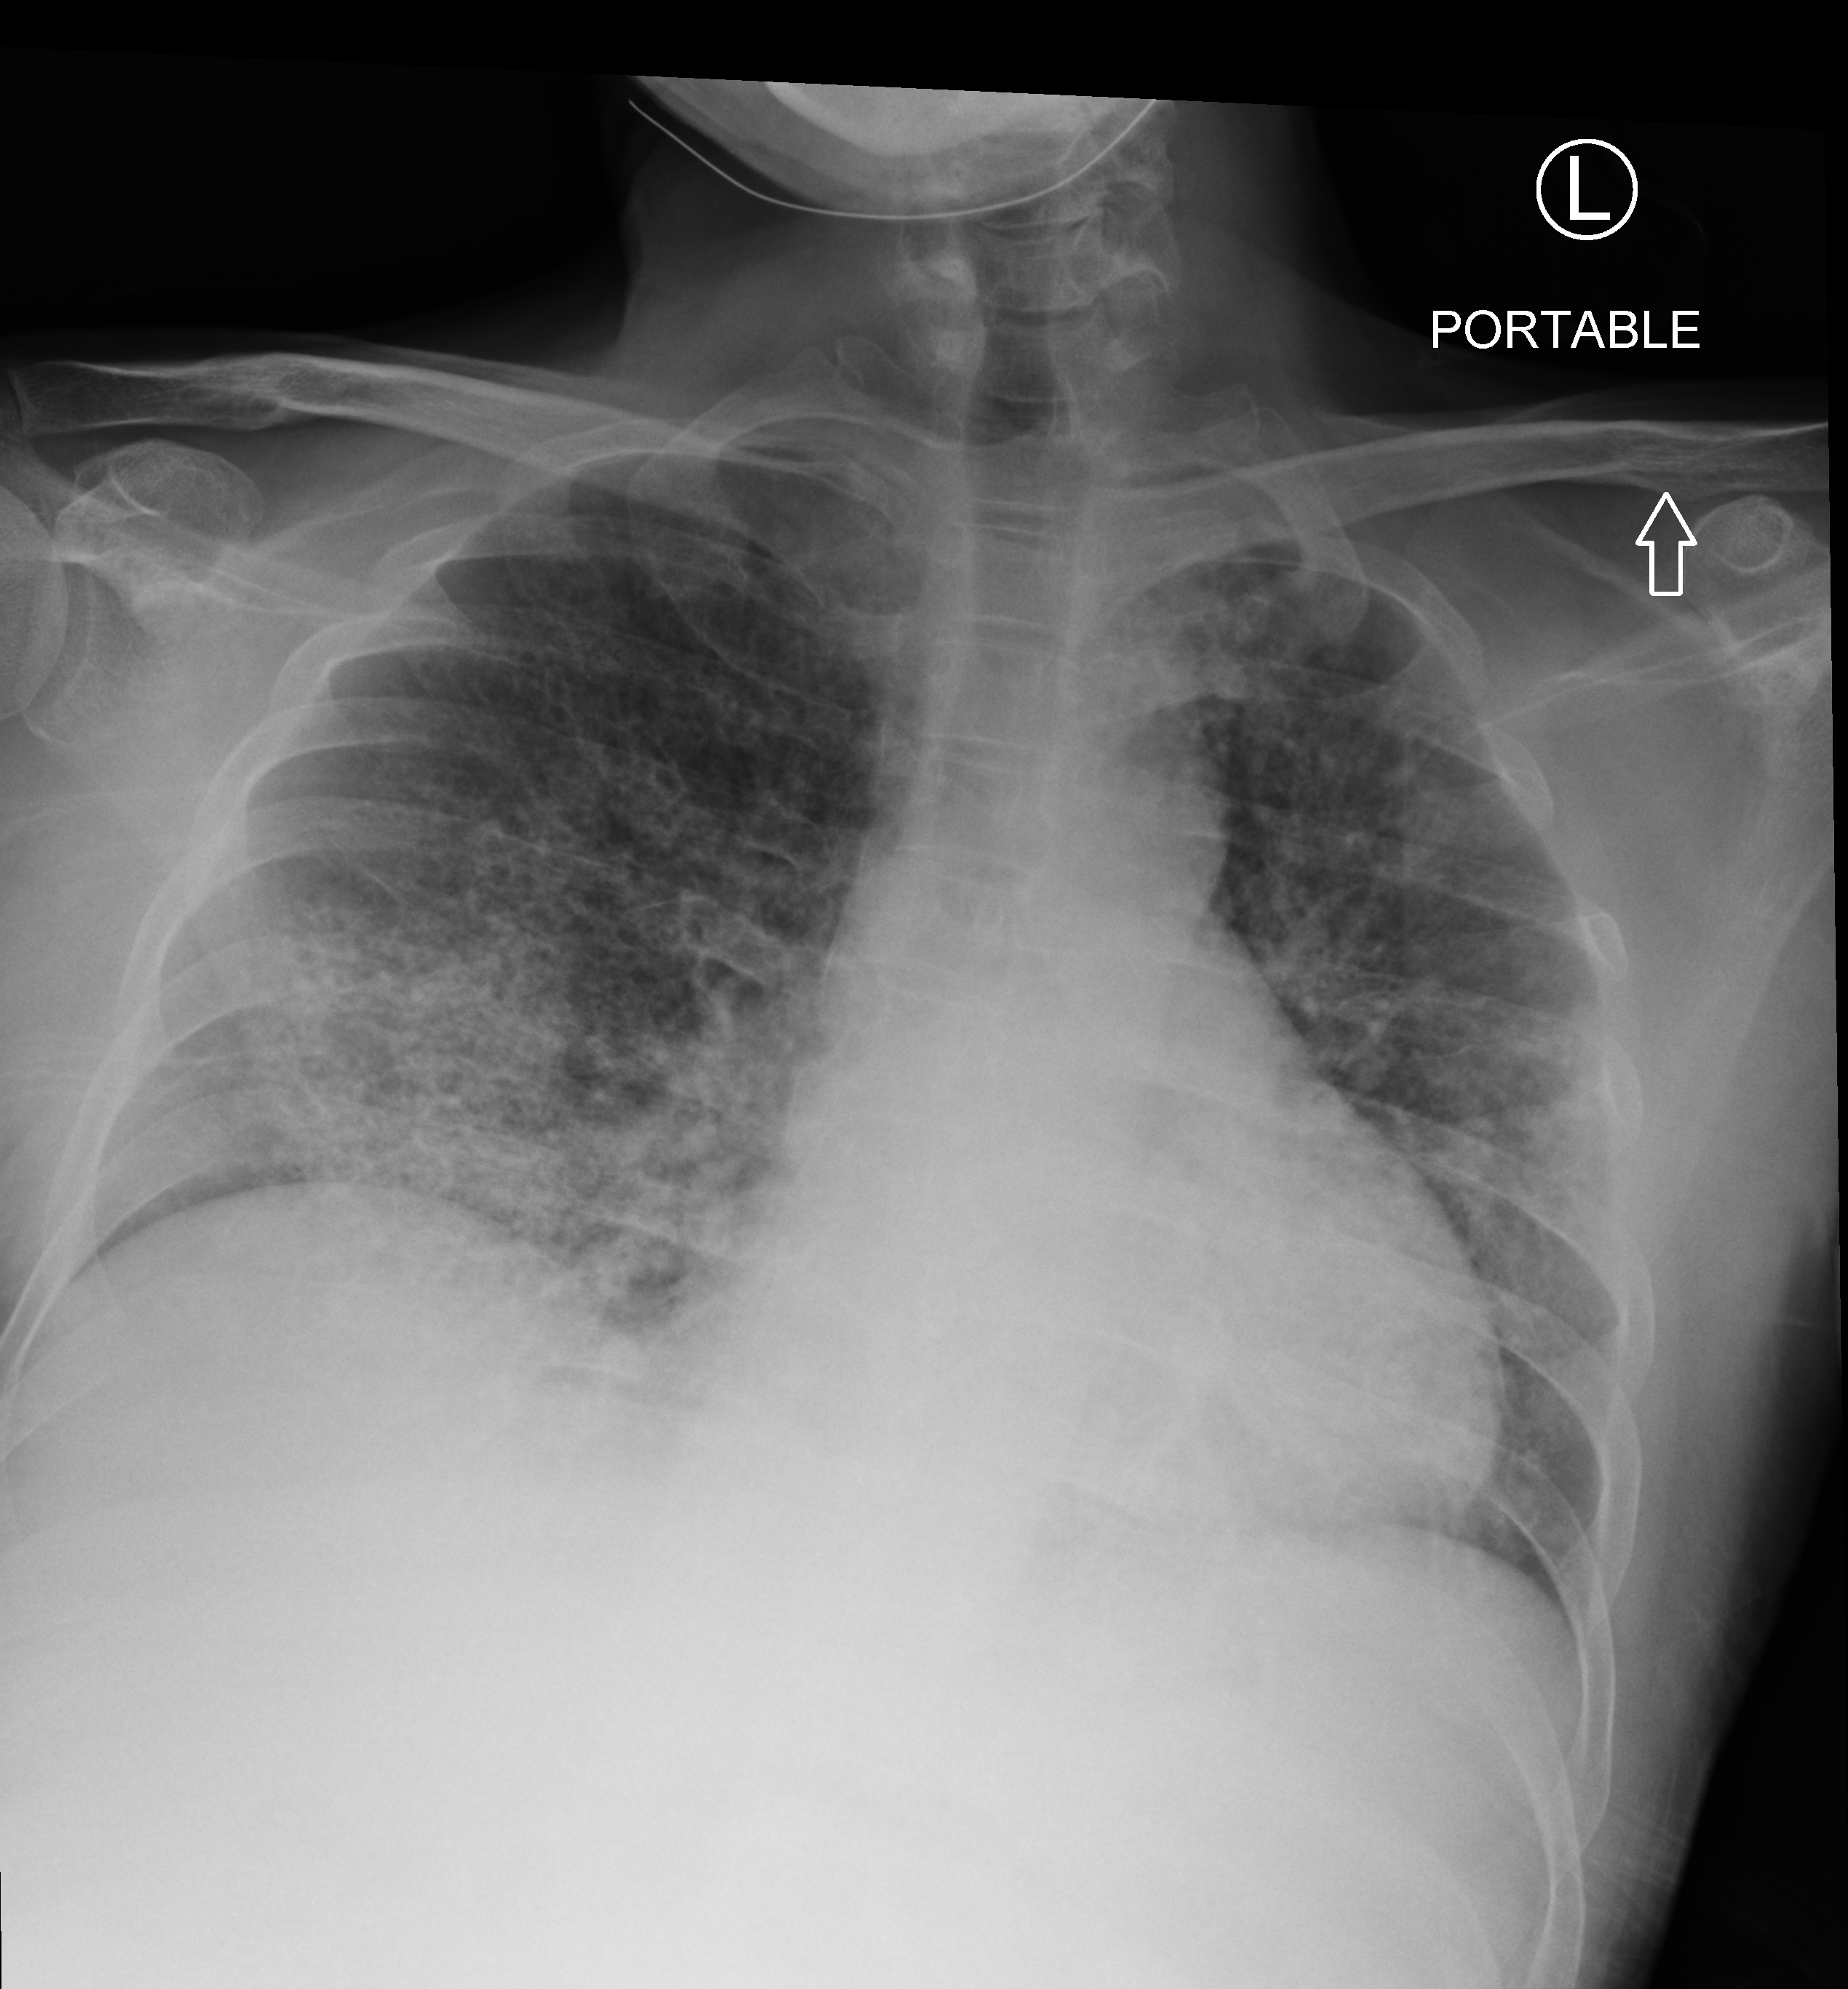
Bedside chest radiograph (computed radiography), anteroposterior (AP) projection. Patient hospitalised with COVID-19; male, aged 18–59 years.
Hospital-stay facts (about this admission, not read from this image; timing relative to this image not recorded):
- COPD (admission record): no
- length of hospital stay: 6 days
- mechanically ventilated during this hospital stay: no